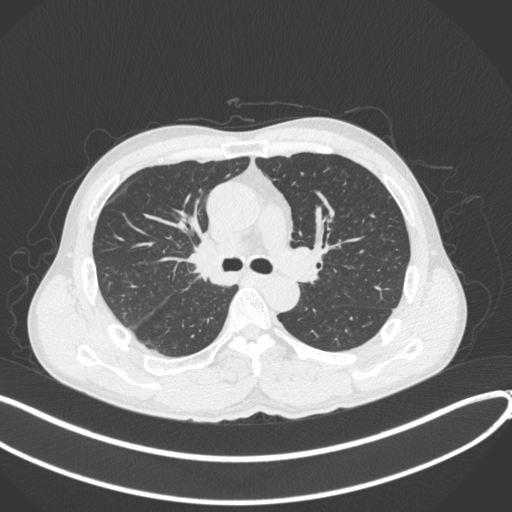
Chest CT, one axial slice; slice 242 of 409 in the series (ordered by position); 120 kVp; lung window (W 1500 / L -600 HU); 1 mm slice thickness; 512 × 512 image matrix. Male patient, age 53 years. From the clinical record (not read from this slice): clinical TNM (as recorded): T1b N0 M0.
Structures marked on this image (rectangle marked by the reading radiologist):
- lung tumour (recorded histology: squamous cell carcinoma): bounding box [x1, y1, x2, y2] px = [183, 232, 233, 290]